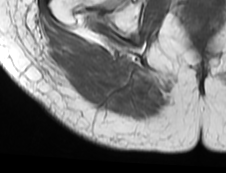
MRI of an extremity soft-tissue mass, one axial slice. Position 23 of 73 along the scan axis. MR volume resampled by the dataset authors to the PET/CT grid (not the native acquisition matrix). 3.27 mm slice thickness. 226 × 173 image matrix, field of view 221 × 169 mm. Female patient. From the clinical record (not read from this slice): histological type: spindle cell suggestive of myxofibrosarcoma; grade: intermediate; site of the primary tumour: right buttock.
Structures marked on this image (expert contour drawn on MRI and transferred to this co-registered scan by the dataset authors):
- gross tumour volume (mass): bounding box (x1, y1, x2, y2) in pixels: (47, 42, 112, 93)